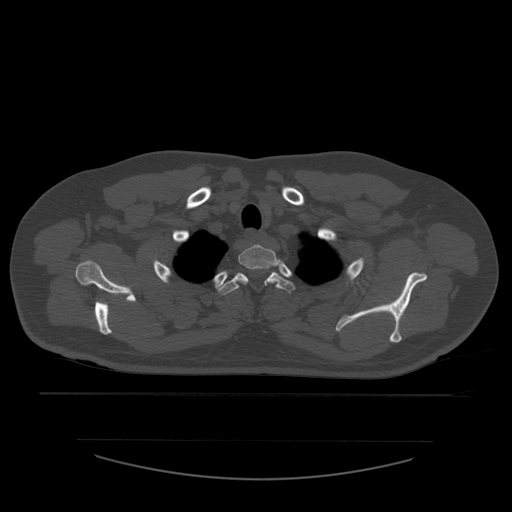
CT including the spine, one axial slice. Position 458 of 532 along the scan axis. Reconstruction kernel STANDARD. Bone window (W 1800 / L 400 HU). 1.25 mm slice thickness. 512 × 512 image matrix, field of view 441 × 441 mm. Patient age 44 years. Case-level facts recorded for this patient, not image findings: primary cancer: soft tissue sarcoma.
Annotated regions visible in this slice (semi-automatically segmented with operator editing):
- T1 vertebra: bounding box [x1, y1, x2, y2] px = [239, 245, 277, 284]
- T2 vertebra: [218, 272, 295, 295]